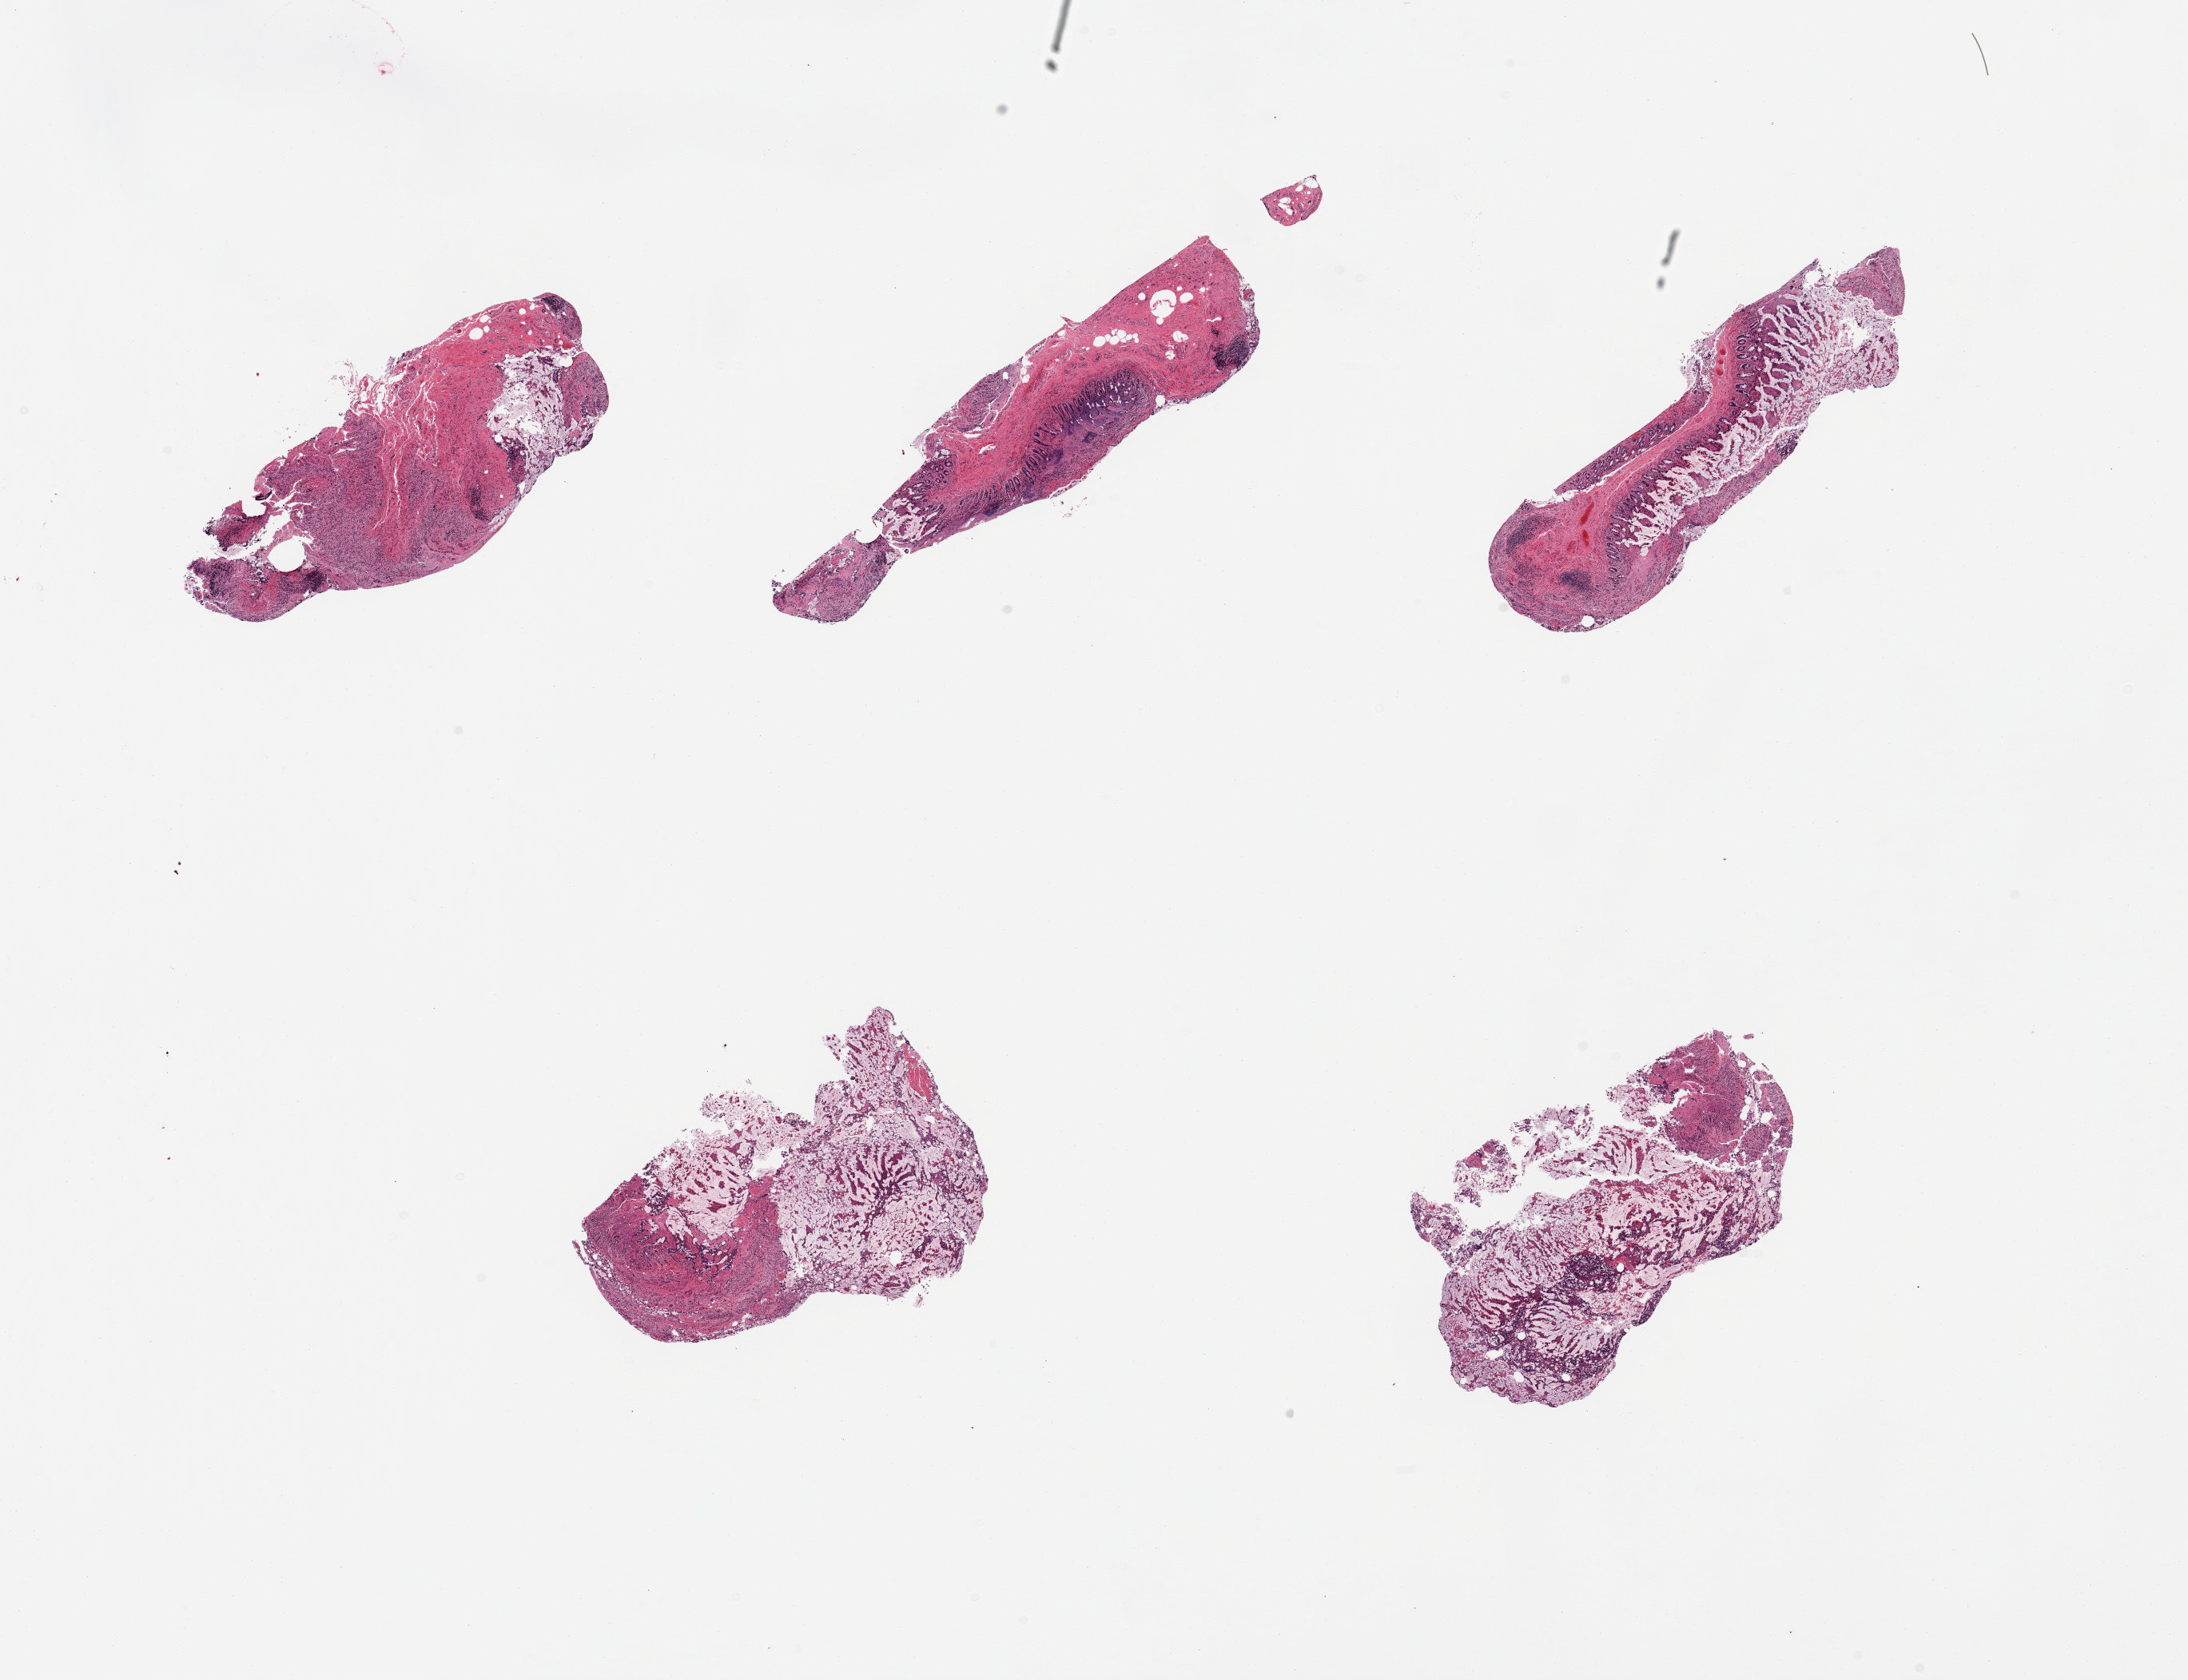
Haematoxylin and eosin whole-slide image, brightfield — whole scanned area (about 21.7 x 16.6 mm, acquisition: 20x scan) shown as a low-resolution overview, PAXgene-fixed paraffin-embedded (PFPE) section, target tissue: ileum, donor tissue sample. Male donor.
• reviewer comment on this tissue sample: 4 pieces, target mucosa but <5% target lymphoid aggregates